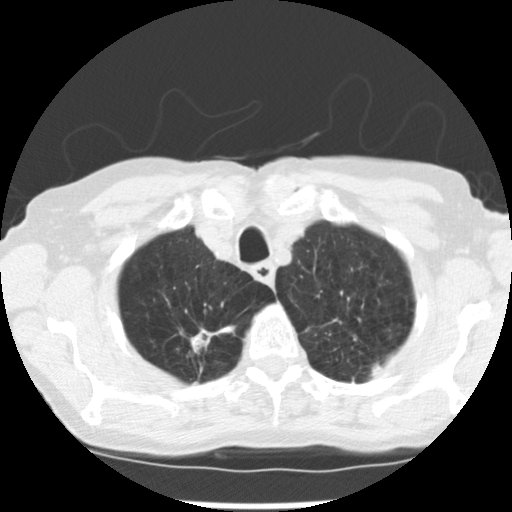
Low-dose screening chest CT, axial slice, baseline screening round, lung window (W 1500 / L -600 HU), 2.5 mm slice thickness, standard (soft-tissue) reconstruction kernel (STANDARD), slice 32 of 265 in the series, 512 × 512 image matrix. Female participant, aged 72 years at enrolment.
• Expert reader's lesion annotation, bounding box [x1, y1, x2, y2] px = [177, 313, 232, 354].
• The screening reader recorded 3 non-calcified nodules or masses ≥4 mm on this exam (right upper lobe, left upper lobe, left lower lobe); which of them this box marks is not recorded.
• Later outcome: lung cancer diagnosed 50 days after this screen — adenocarcinoma, NOS, right upper lobe, moderately differentiated (G2), stage IB (AJCC 6th edition), 22 mm at pathology.